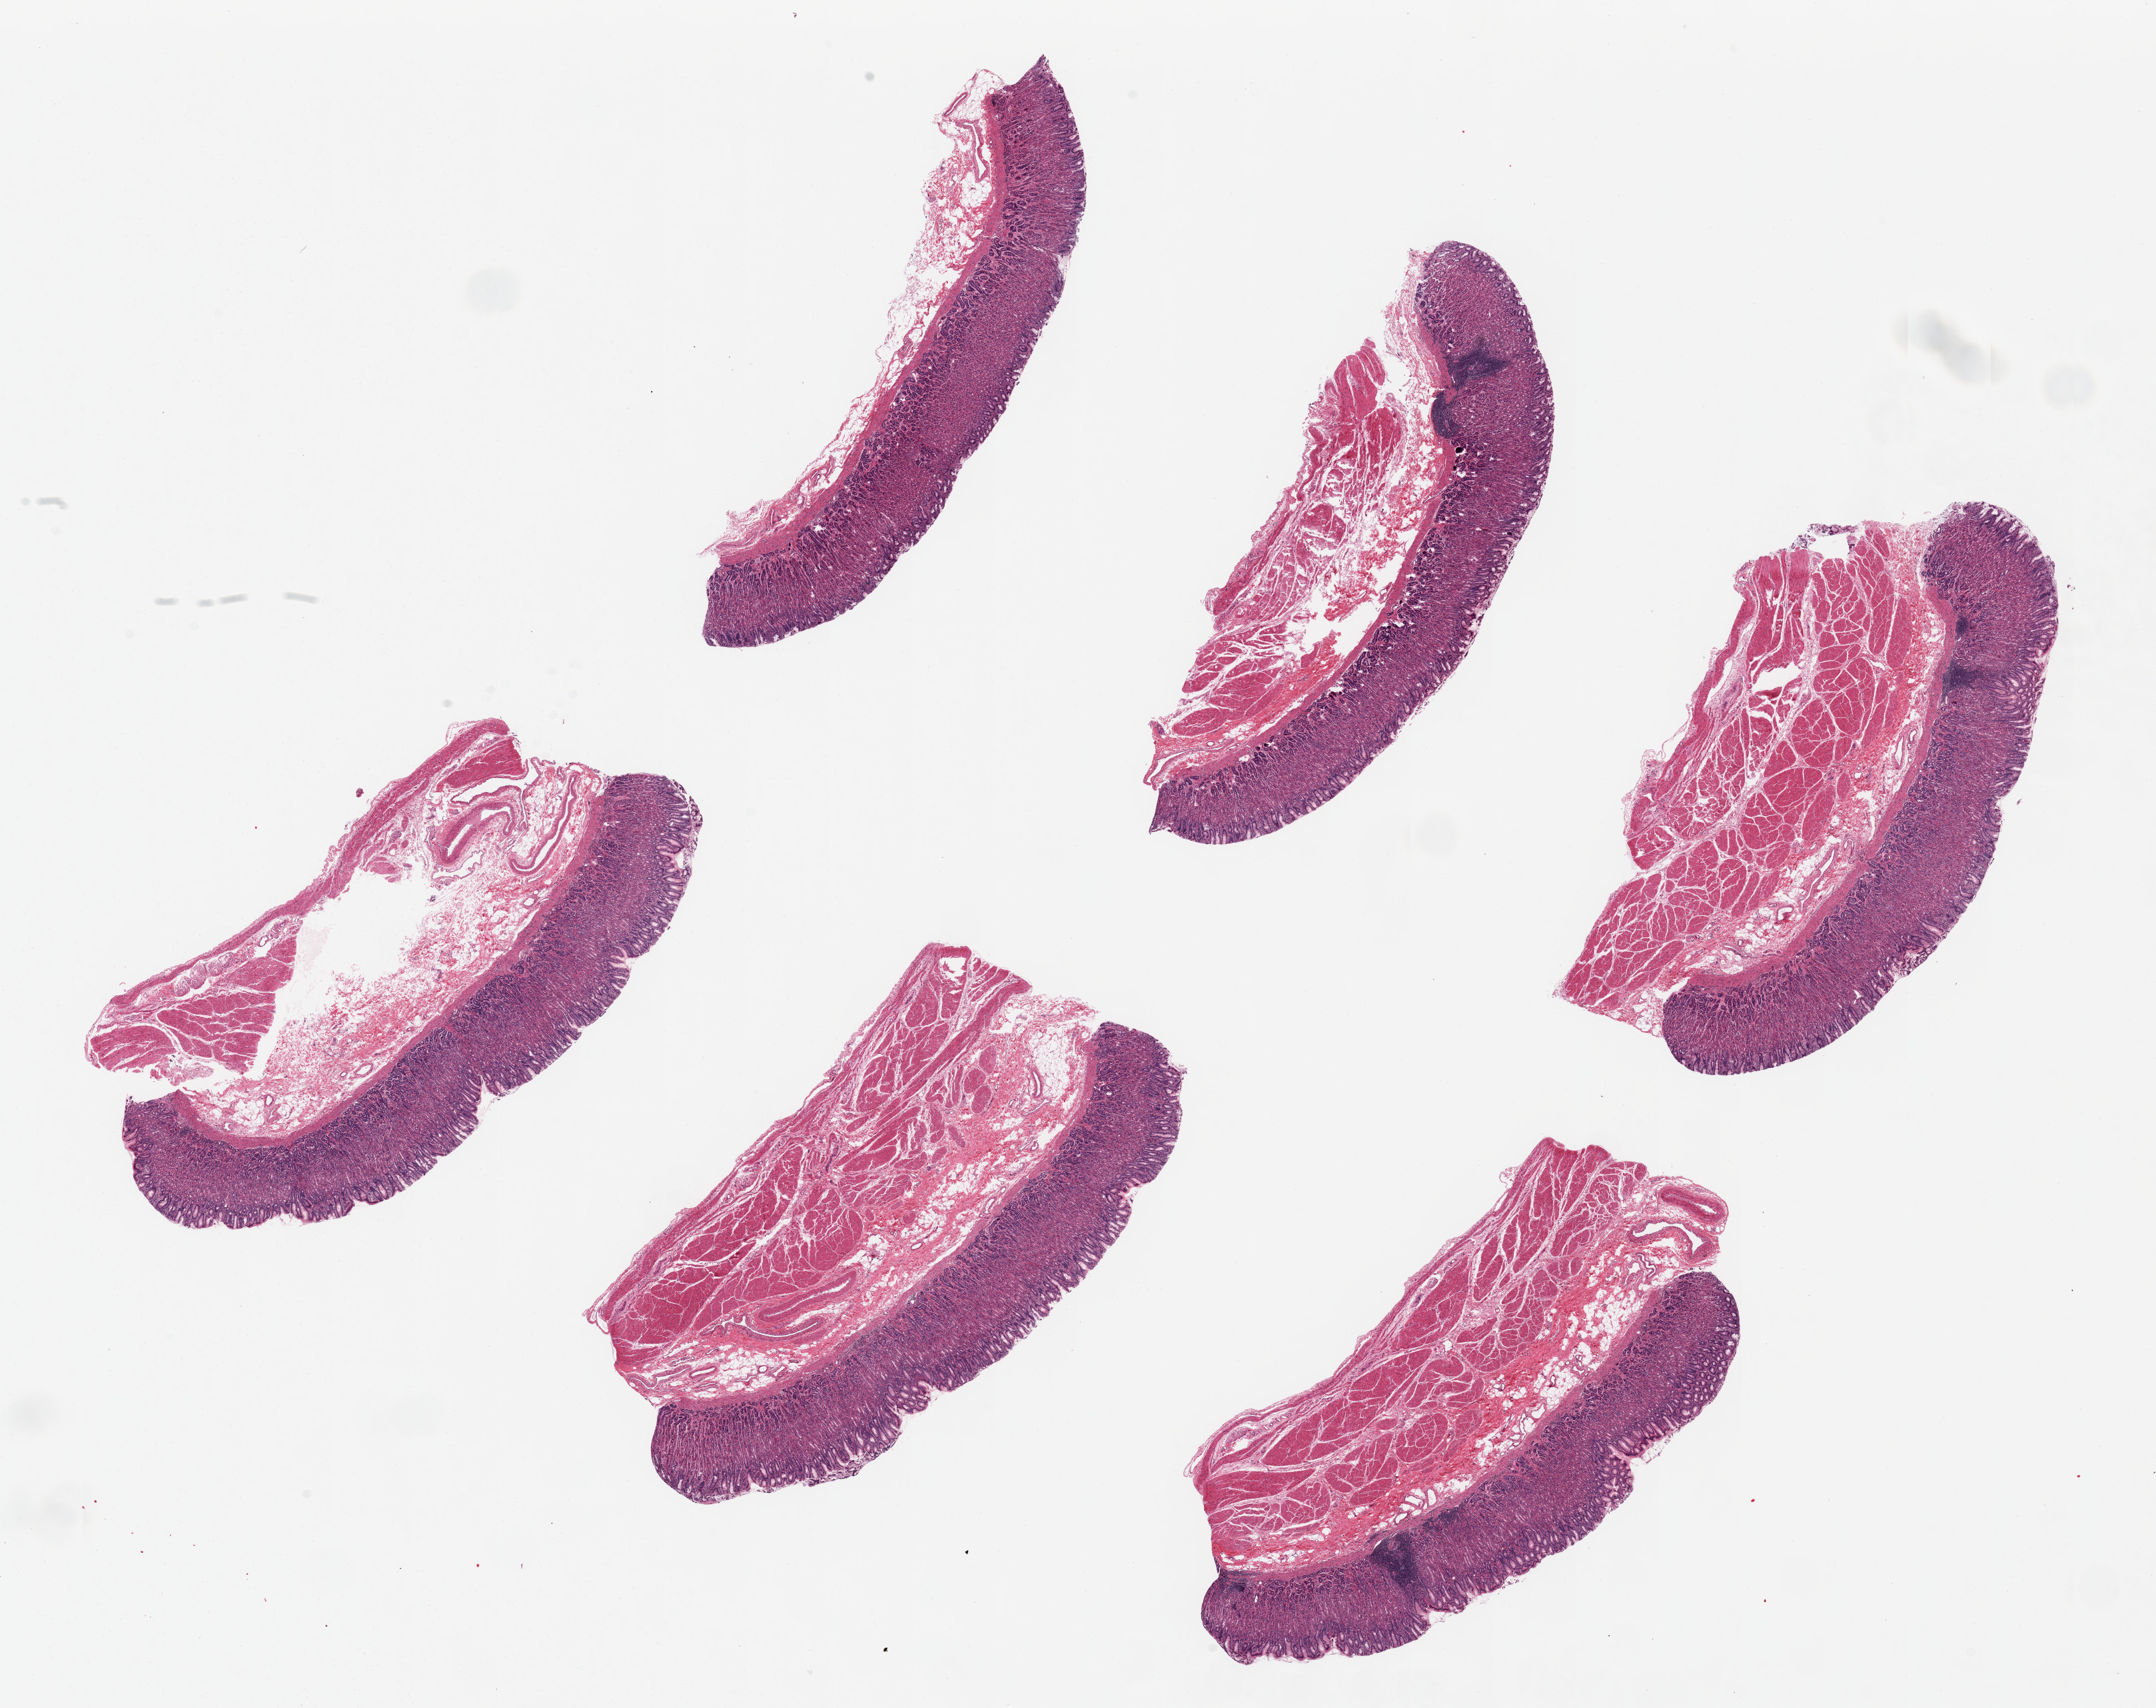
Digitized haematoxylin and eosin-stained section, brightfield, shown as a low-resolution overview of the whole scanned area (about 25.6 x 20.3 mm), PAXgene-fixed, paraffin-embedded tissue, sampled site (target tissue): stomach, tissue donor sample. Donor: female.
* pathologist's review note for this sample: 6 ~7x3.5mm pieces. Mucosa overall well-preserved, focally with superficial moderate autolysis. Chronic gastritis (patchy). Mucosa ranges from ~30-60% of thickness